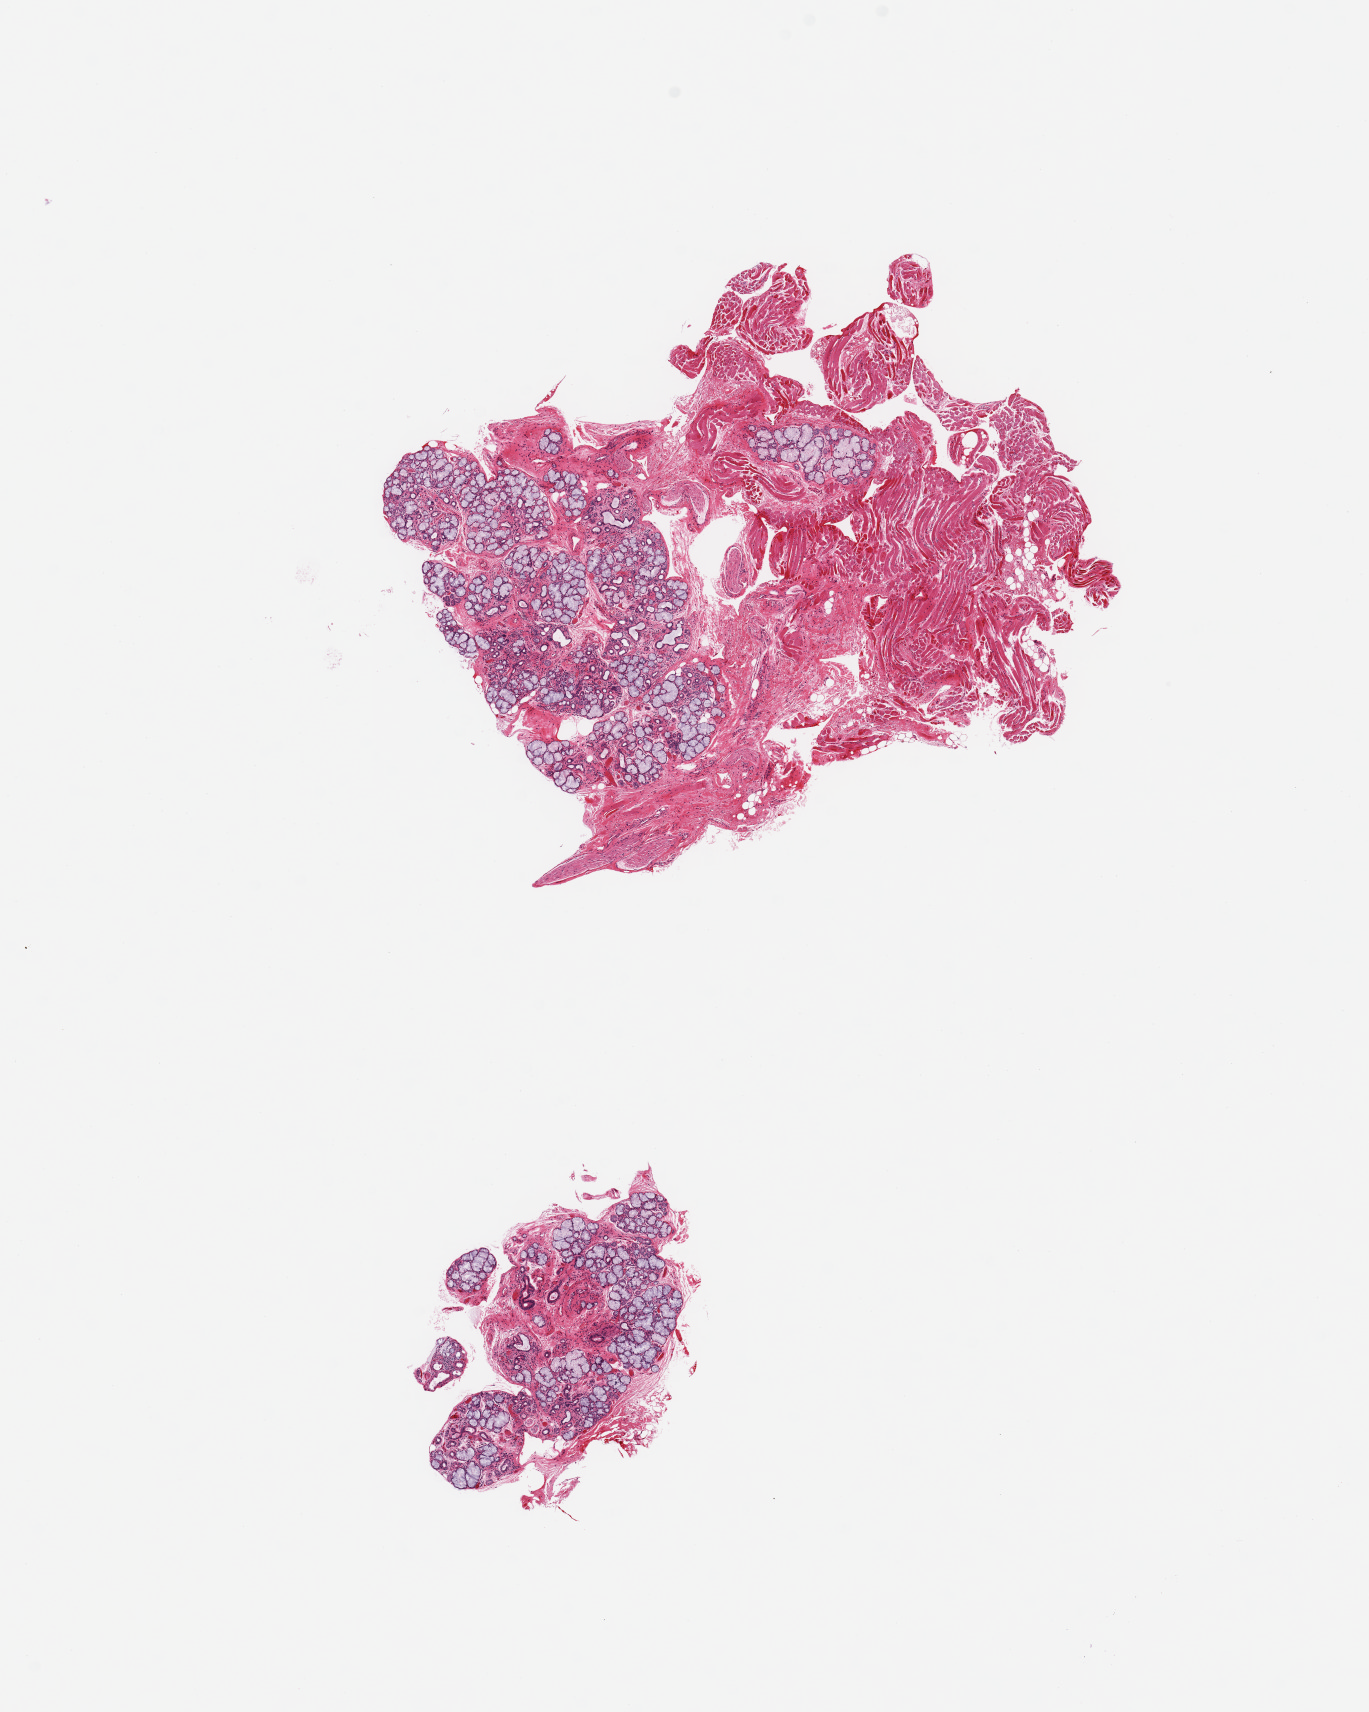
Haematoxylin and eosin whole-slide image, brightfield — shown as a low-resolution overview of the whole scanned area (about 10.8 x 13.5 mm, from a 20x scan); PAXgene-fixed, paraffin-embedded tissue; sampled site (target tissue): minor salivary gland; donor tissue sample. Male donor.
* pathologist's review note for this sample: 2 pieces, ~50% glandular elements; sample with care